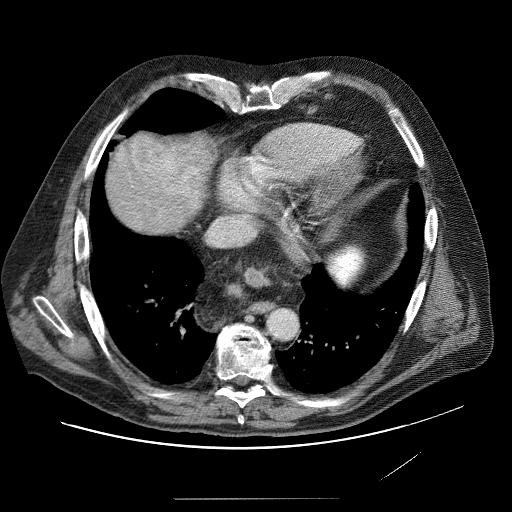
Contrast-enhanced abdominal CT (liver protocol), one axial slice; position 78 of 89 along the scan axis; reconstruction kernel STANDARD; soft-tissue window (W 400 / L 40 HU); 2.5 mm slice thickness; 512 × 512 image matrix. Case-level facts recorded for this patient, not image findings: diagnosis: hepatocellular carcinoma (patient treated with transarterial chemoembolisation; whether this scan precedes or follows treatment is not stated here); TNM stage (as recorded): Stage-IVA.
Annotated regions visible in this slice (semi-automatically segmented with operator editing):
- liver parenchyma outside the tumour (the mass and vessels are separate outlines, so this box may not span the whole liver): box from (x=114, y=136) to (x=195, y=216) px
- mass: (x=131, y=137)–(x=186, y=194)
- liver vessels: (x=154, y=197)–(x=158, y=200)